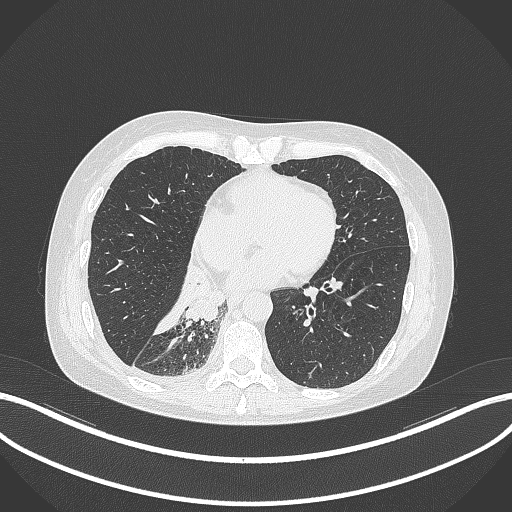
Chest CT, one axial slice; position 115 of 329 along the scan axis; reconstruction kernel B70f; 120 kVp; lung window (W 1500 / L -600 HU); 512 × 512 image matrix, field of view 400 × 400 mm. Patient: female, 63 years. Case-level facts recorded for this patient, not image findings: clinical TNM (as recorded): T1c N0 M0.
Outlined on this slice (rectangle marked by the reading radiologist):
- lung tumour (recorded histology: adenocarcinoma): bounding box (x1, y1, x2, y2) in pixels: (176, 261, 229, 327)